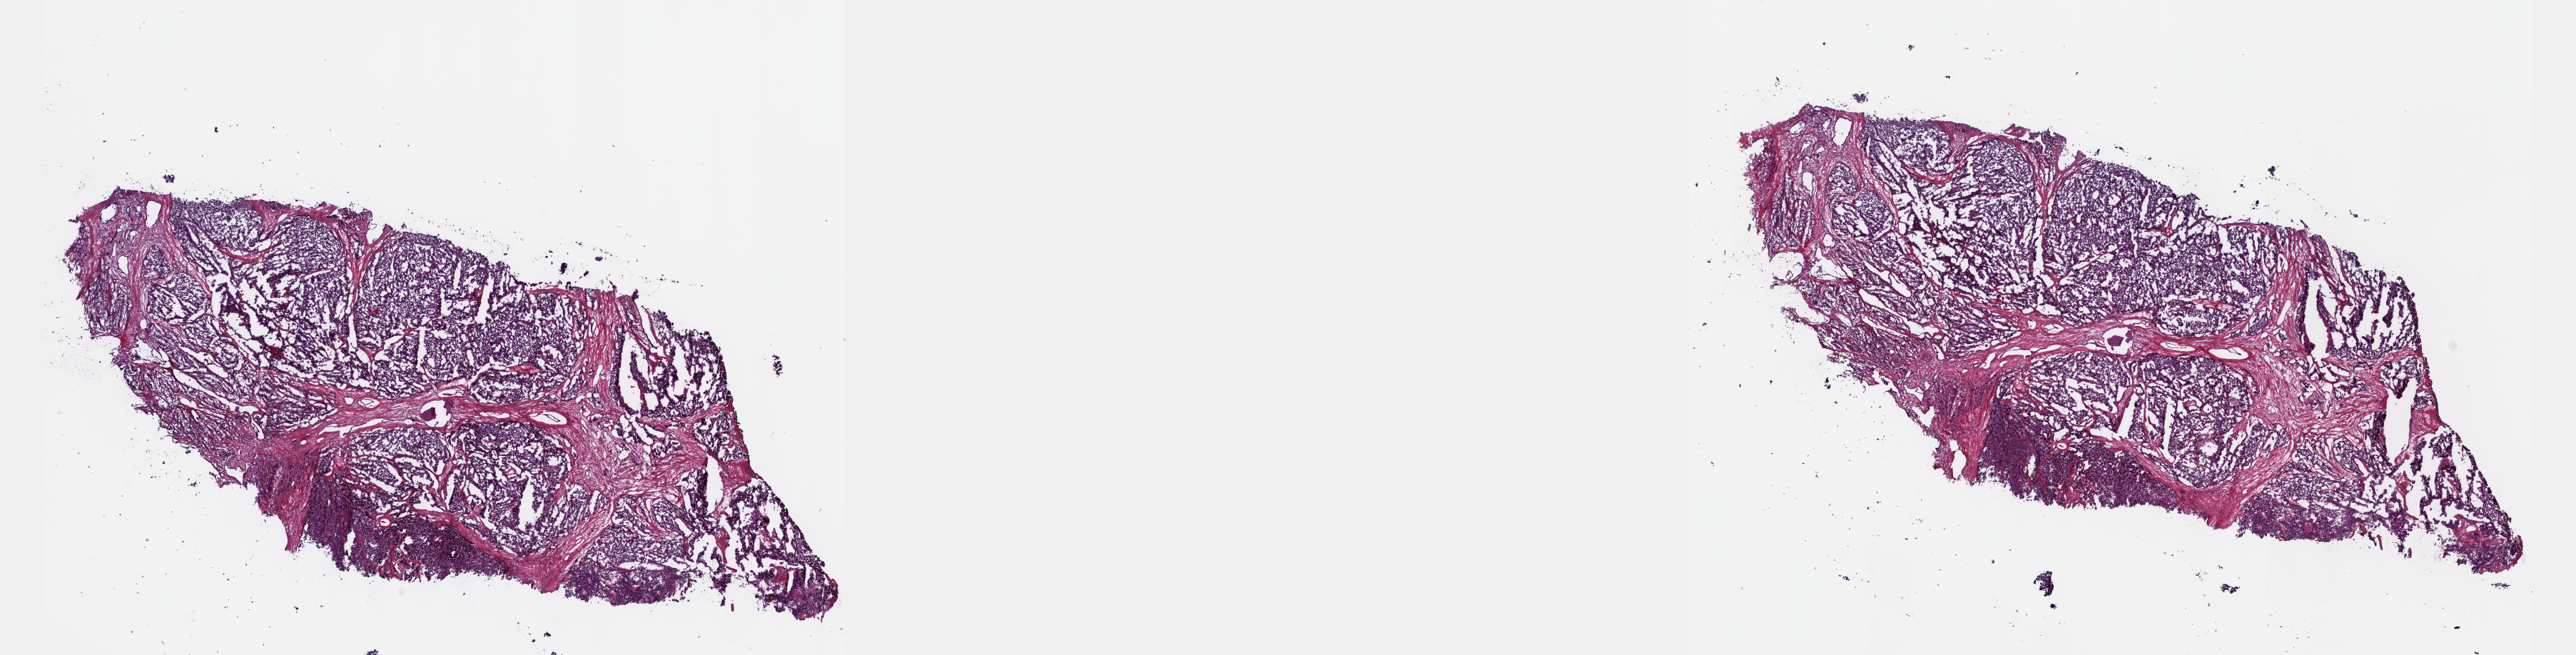
Digitized Hematoxylin and eosin (H&E) stained tissue section (whole slide), whole scanned area (about 29.2 x 7.4 mm, from a 40x scan) shown as a low-resolution overview; frozen section from the top of the tissue portion; primary tumour sample from the prostate. Male, age 71 years at initial diagnosis. Gleason score: 9 (5+4). Slide review estimates, as recorded: tumour cells 80%, tumour nuclei 90%, normal cells 0%, stromal cells 20%, necrosis 0%. Inflammatory infiltration, as recorded: lymphocyte infiltration 0%, monocyte infiltration 0%, neutrophil infiltration 0%.
- histologic diagnosis: Adenocarcinoma, NOS
- lymph nodes positive (case pathology): 7 of 20 examined